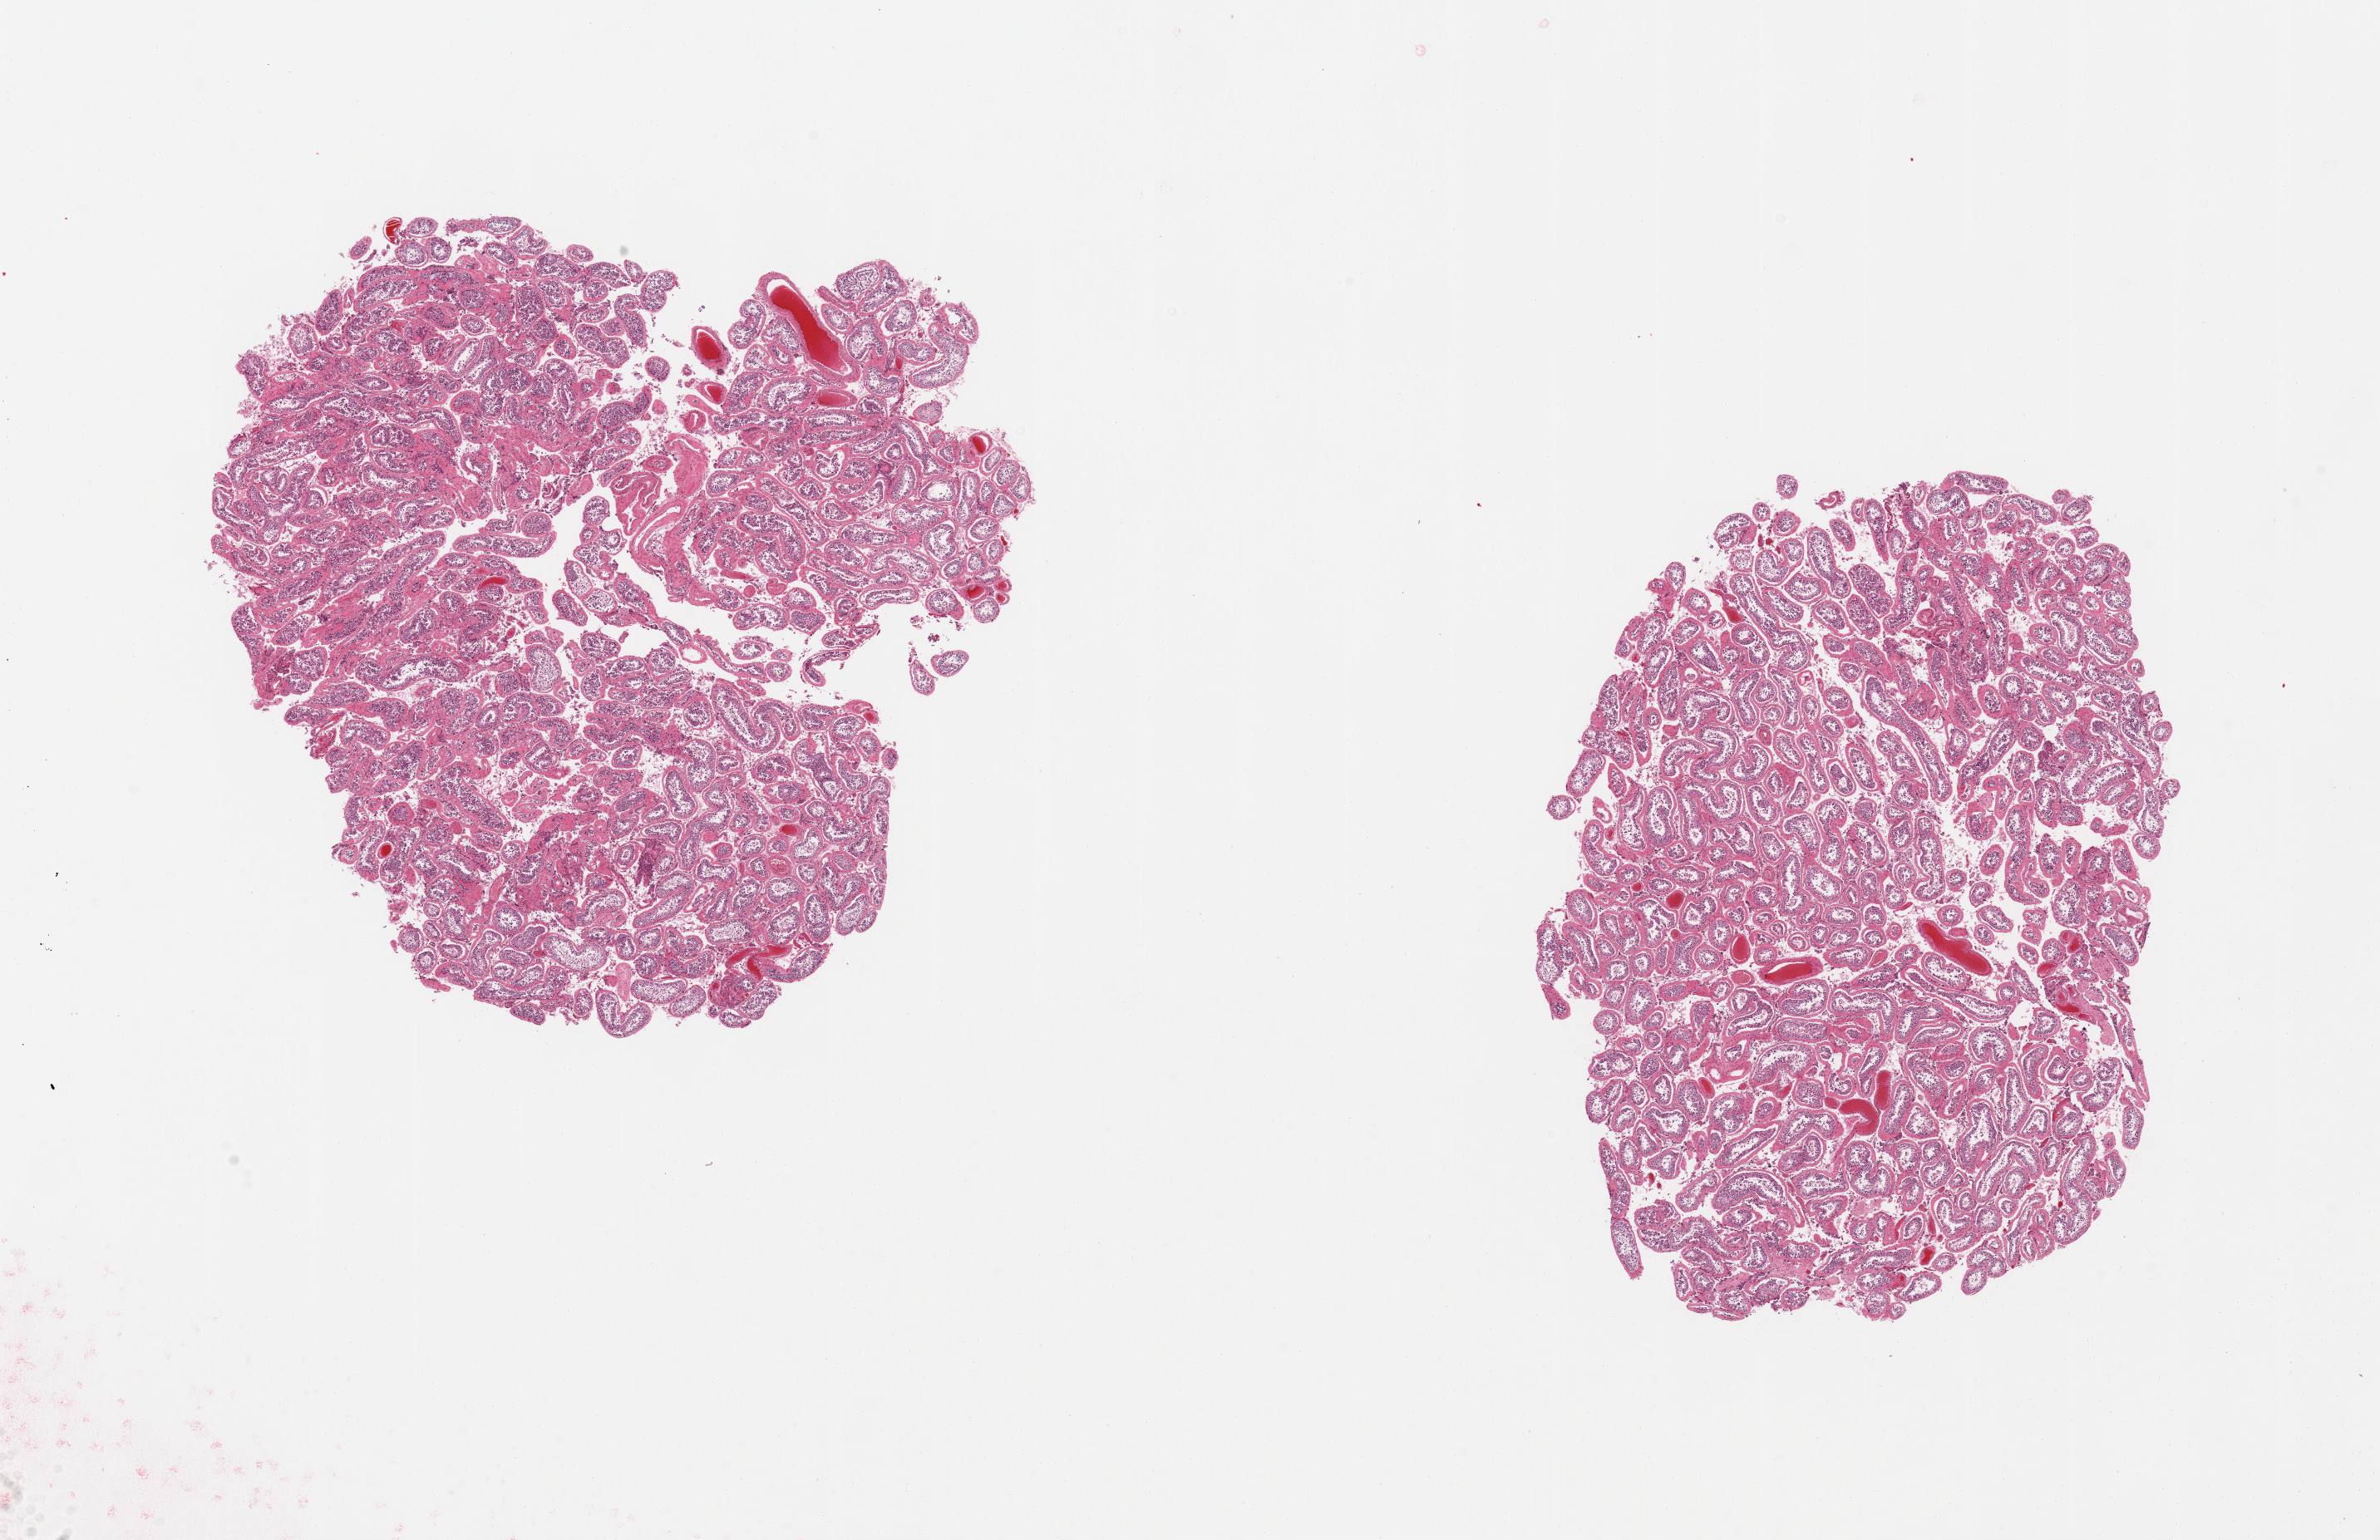
Whole-slide image, hematoxylin and eosin (H&E) stain, brightfield — shown as a low-resolution overview of the whole scanned area (about 22.6 x 14.7 mm, acquisition: 20x scan), PAXgene-fixed, paraffin-embedded tissue, sampled site (target tissue): testis, donor tissue sample. Donor: male.
Review note (as recorded): 2 pieces; slight reduction in mature spermatogenesis.